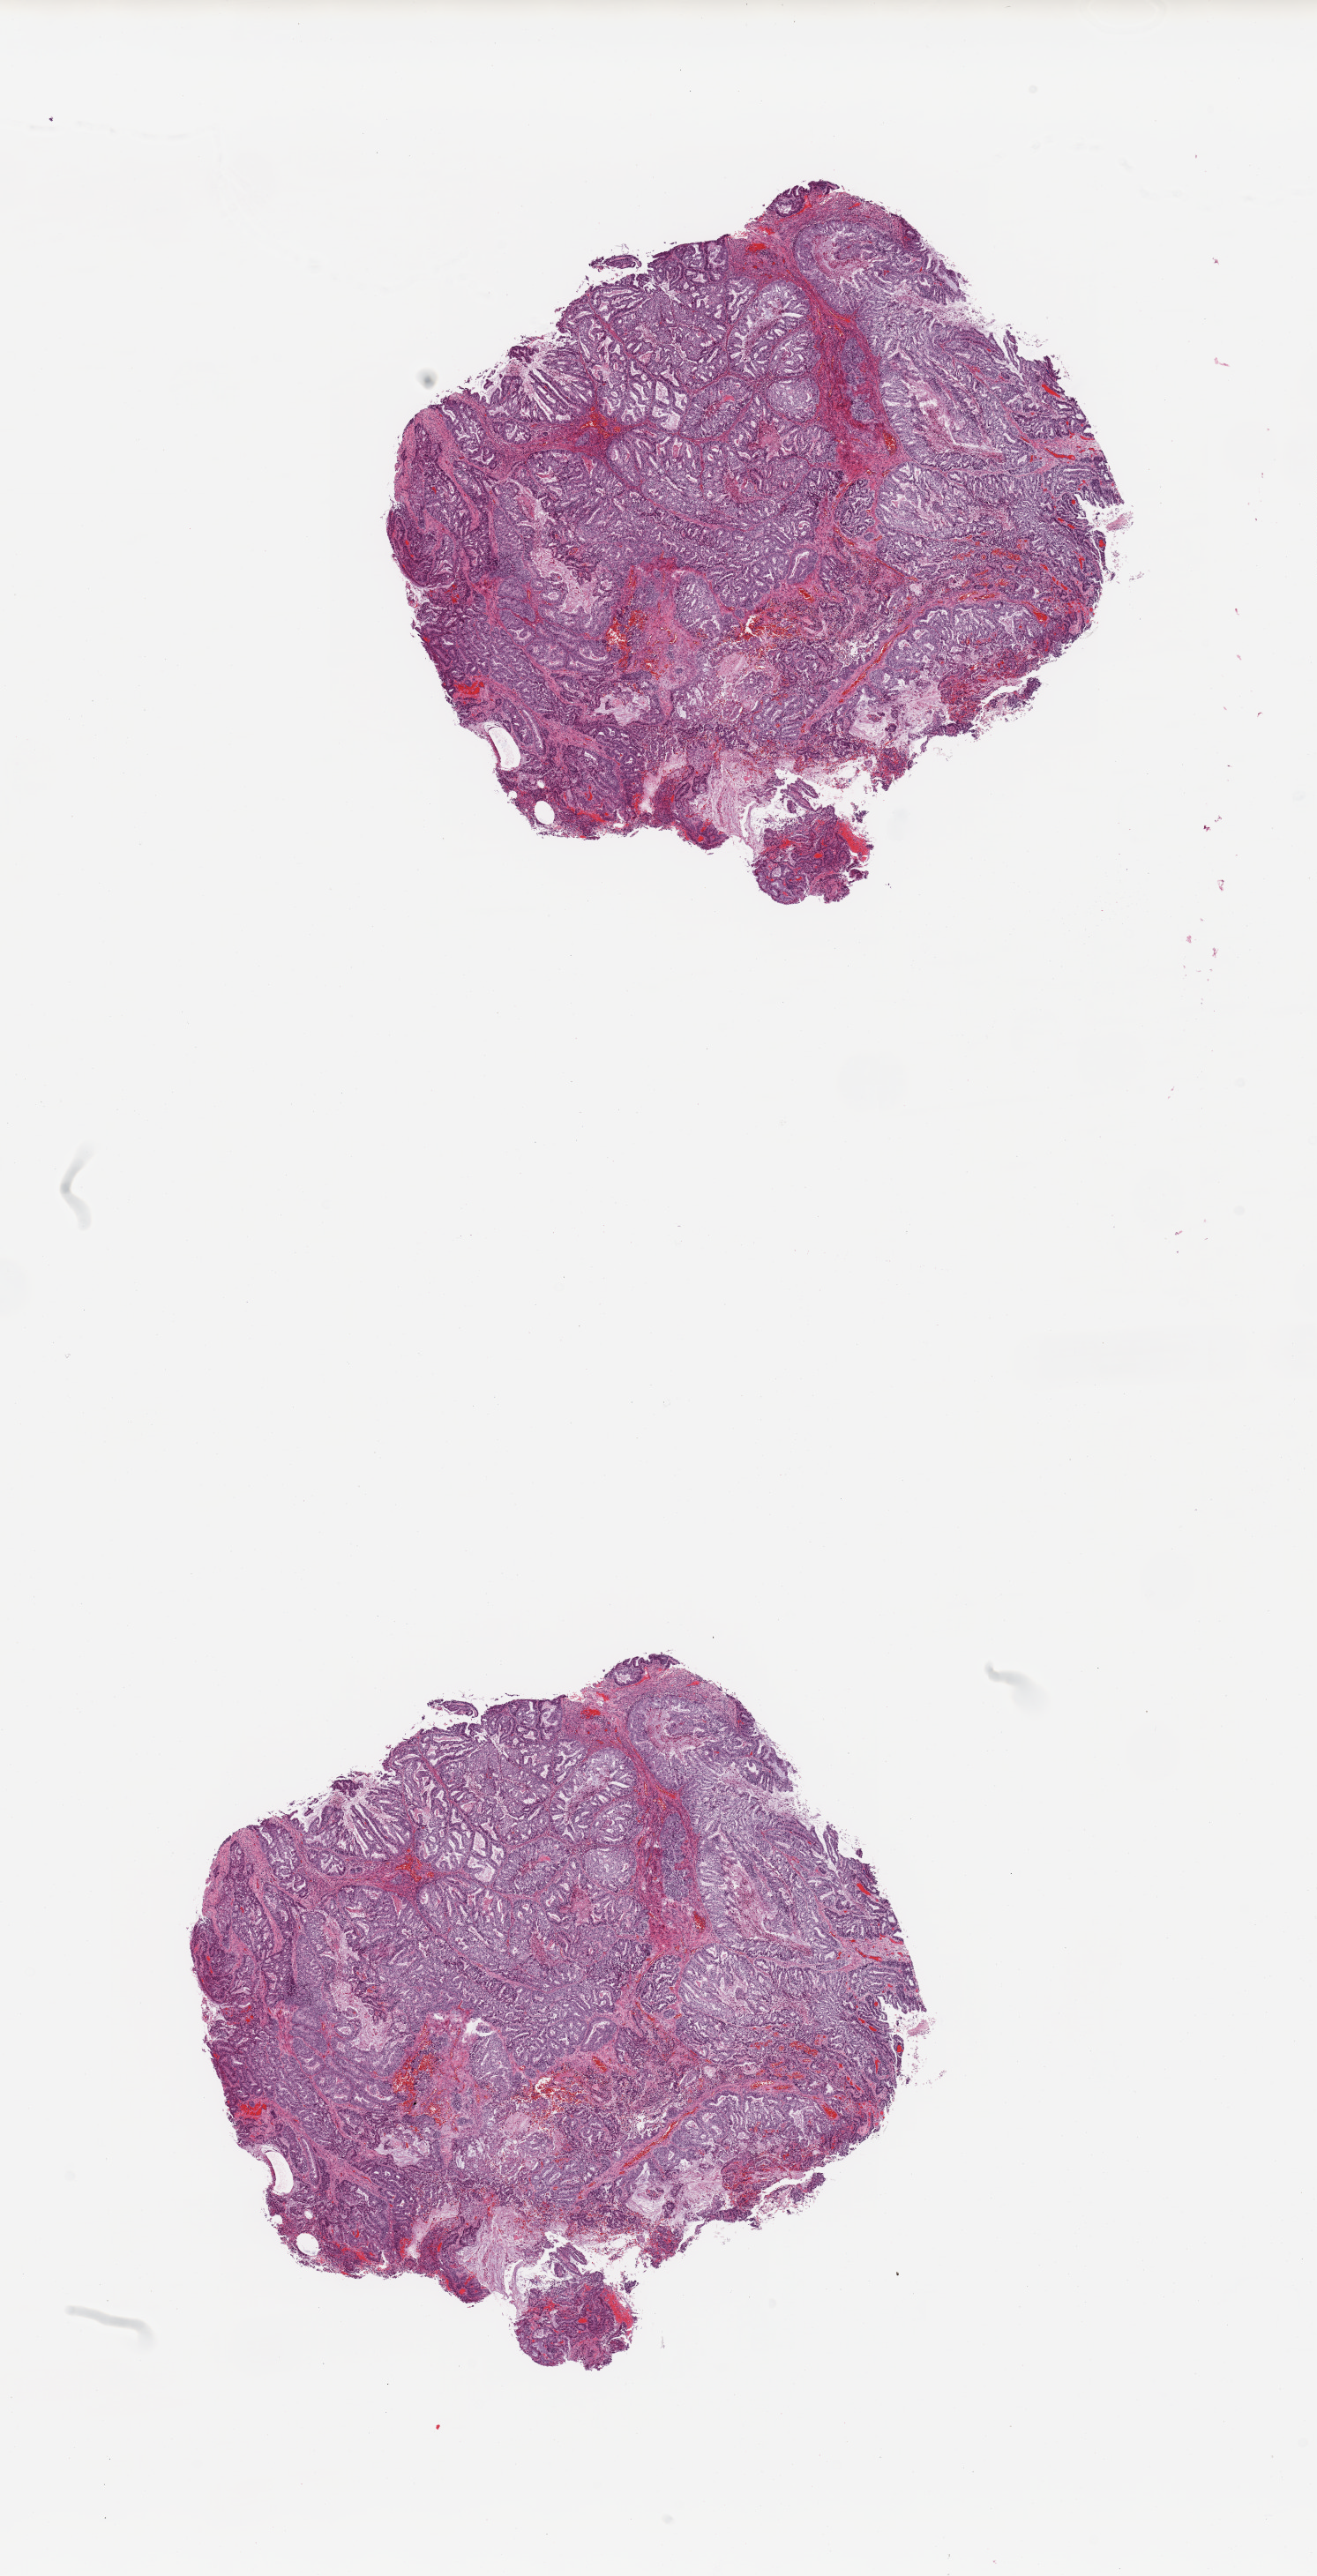
Digitized H&E-stained tissue section (whole slide) — shown as a low-resolution overview of the whole scanned area (about 11.8 x 23.1 mm, acquisition: 20x scan). Tumour tissue sample, sampled site: uterus. Patient: female, age 58 years. Histologic grade: G1 (well differentiated). Pathologist review of this section (percent, as recorded): tumour nuclei 95%, necrosis 1%.
- AJCC pathologic stage: I
- diagnosis: Endometrioid adenocarcinoma, NOS
- primary tumour site (as recorded): posterior endometrium